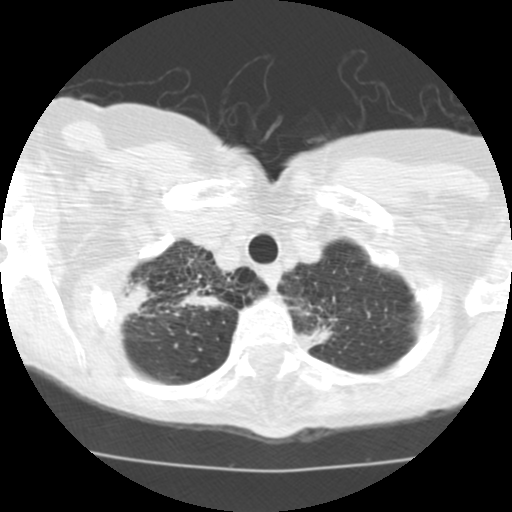
Chest CT (low-dose screening protocol), one axial image. Second annual screen. Lung window (W 1500 / L -600 HU). Standard (soft-tissue) reconstruction kernel (STANDARD). Female participant, aged 68 years at enrolment.
- Expert-annotated lung lesion, box from (x=104, y=263) to (x=164, y=334) px.
- The screening reader recorded 3 non-calcified nodules or masses ≥4 mm on this exam; which of them this box marks is not recorded.
- Participant outcome: lung cancer diagnosed 36 days after this screen — large cell neuroendocrine carcinoma, right upper lobe, undifferentiated (G4), stage IB (AJCC 6th edition), 22 mm at pathology.